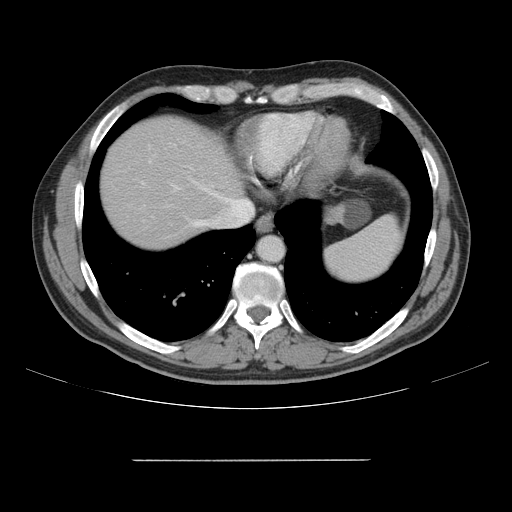
Contrast-enhanced abdominal CT, one axial slice; 120 kVp; intravenous contrast given; soft-tissue window (W 400 / L 40 HU); 2.5 mm slice thickness; 512 × 512 image matrix, field of view 404 × 404 mm. Male patient, age 54 years. From the clinical record (not read from this slice): diagnosis: colorectal cancer liver metastases, imaged before liver resection; multiple liver metastases: yes; largest metastasis: 1 cm; disease in both lobes: no.
Annotated regions visible in this slice (manually delineated by an expert):
- hepatic veins: bounding box <172,179,253,227> (left, top, right, bottom; pixels)
- liver: <101,119,242,249>
- planned liver remnant (the part of the liver to remain after resection): <101,119,241,249>